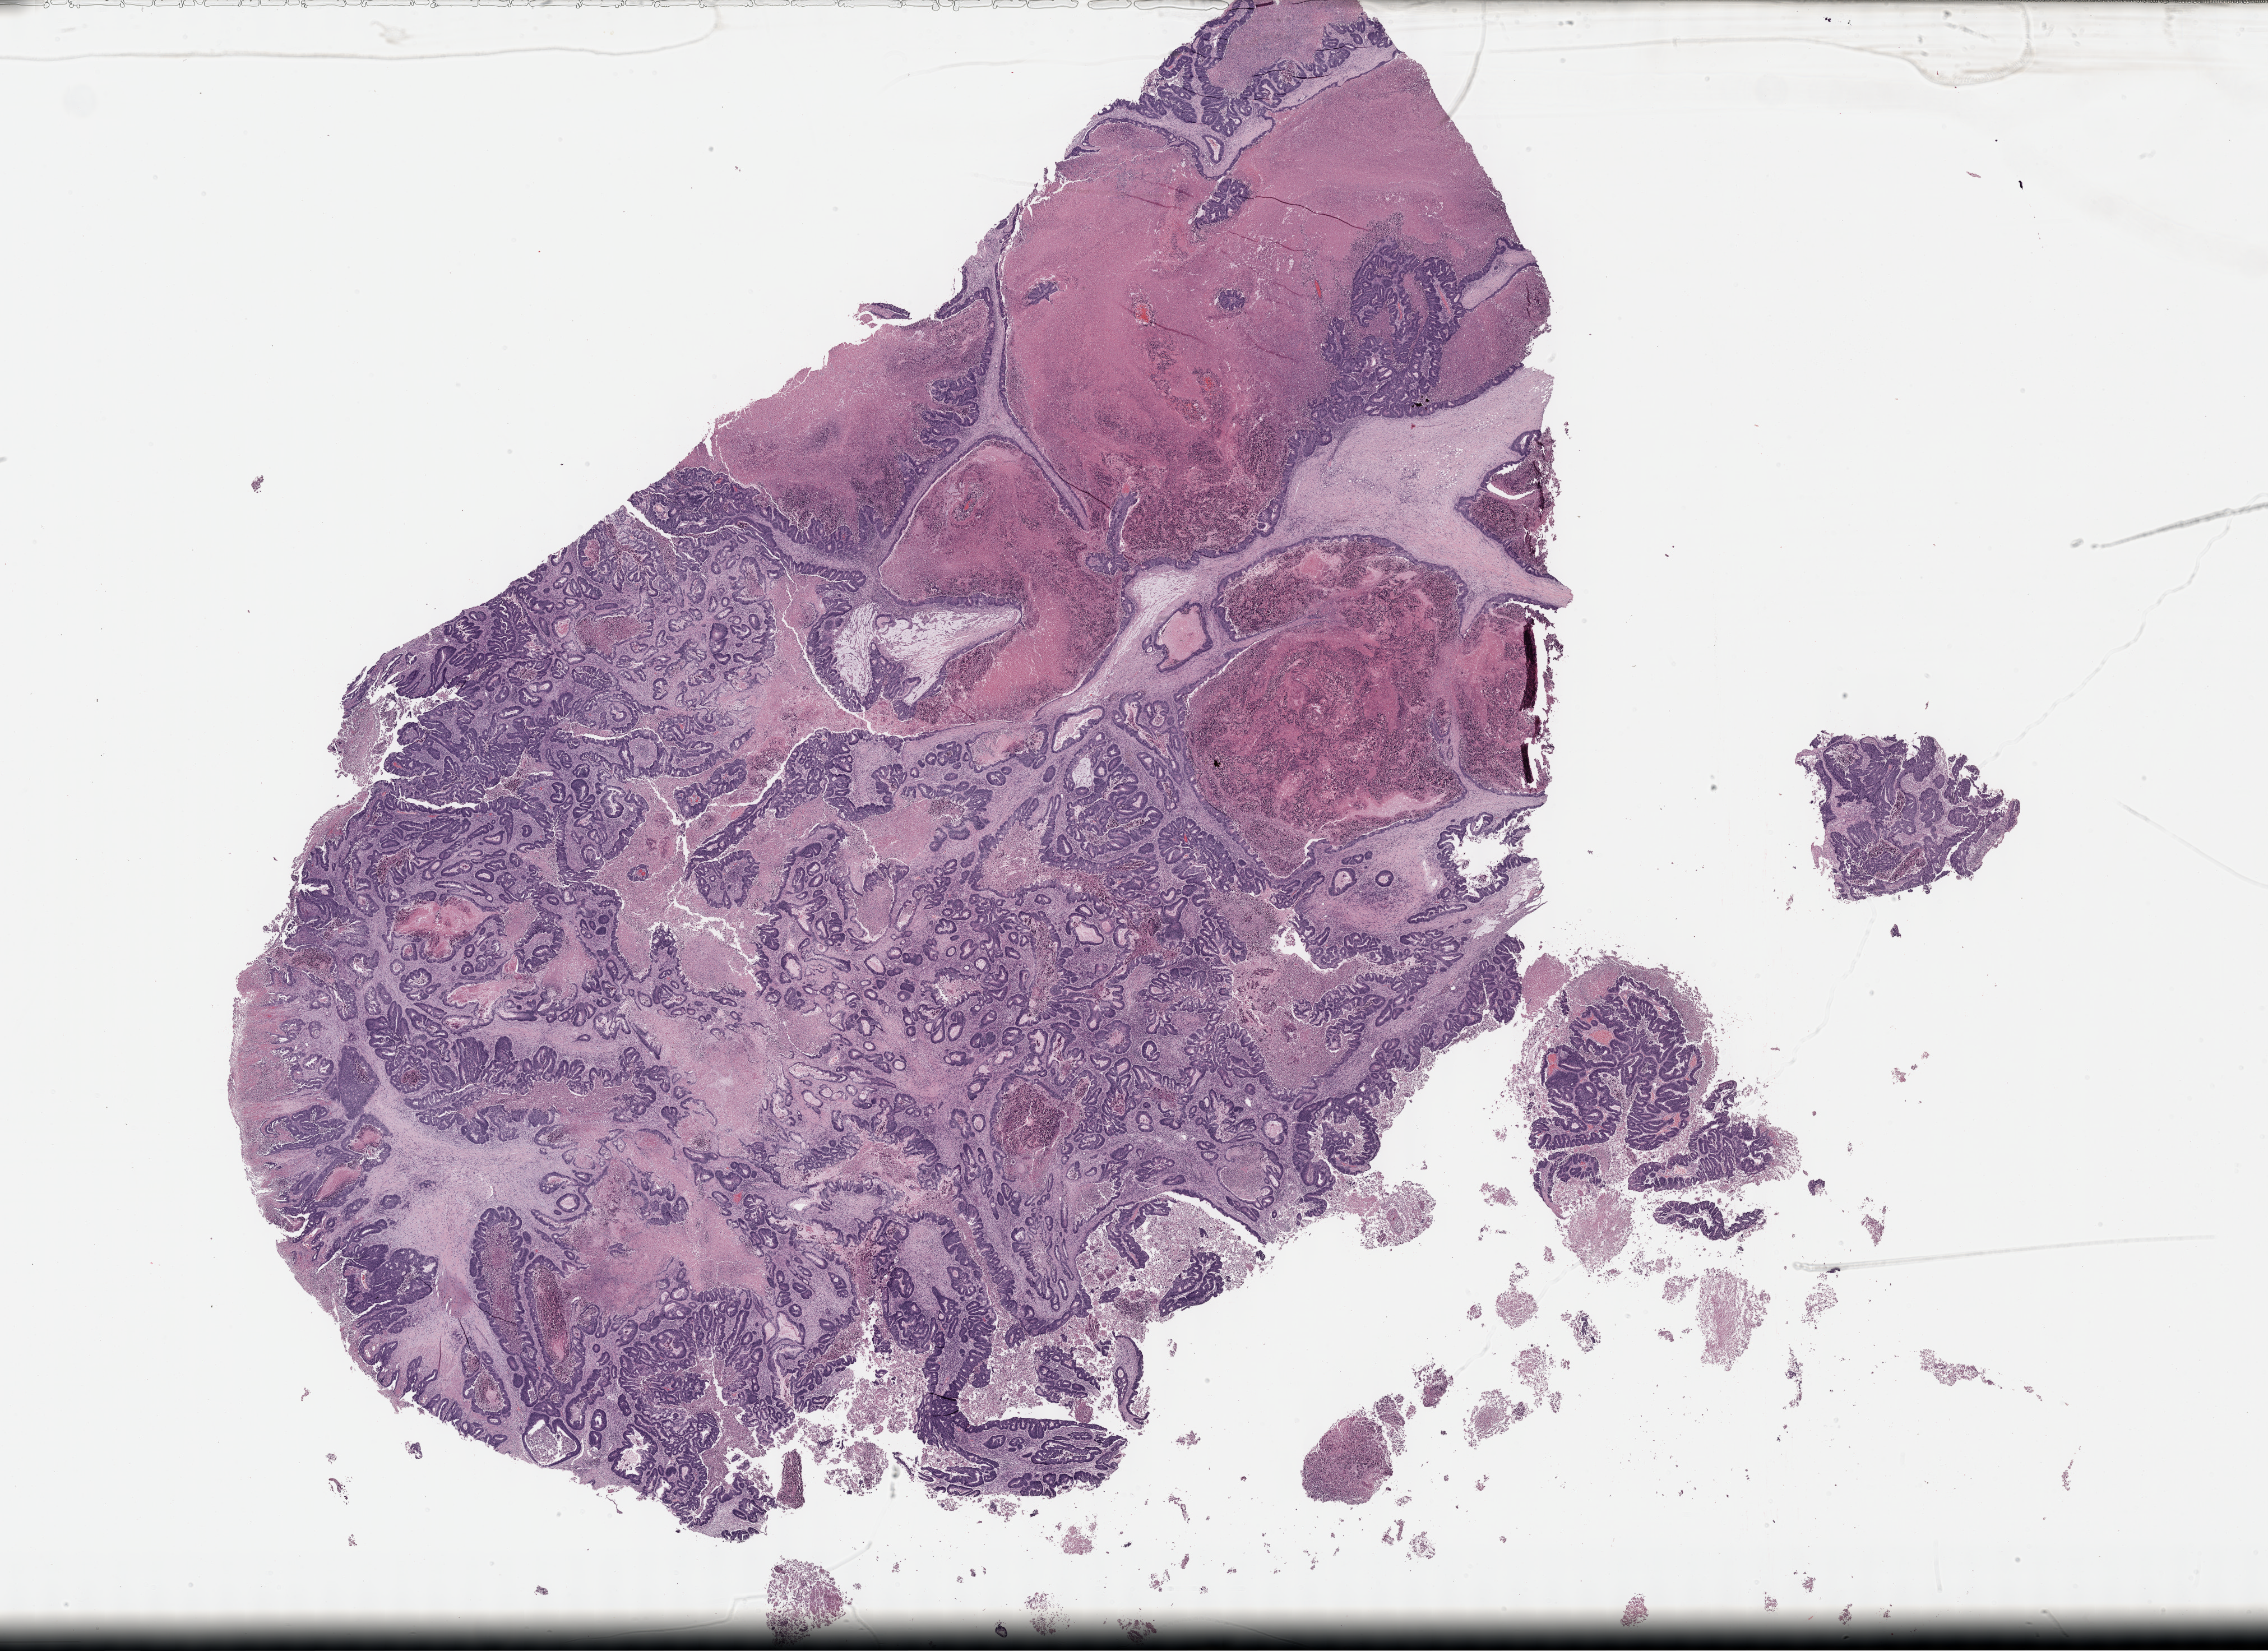
Digitized H&E-stained tissue section (whole slide) — low-resolution overview of the scanned area, about 32.7 x 23.8 mm (acquisition: 40x scan), formalin-fixed paraffin-embedded (FFPE) diagnostic section, primary tumour sample from the colon. Patient: female, age at initial diagnosis 64 years.
AJCC pathologic stage: IIIC (7th edition). Pathologic diagnosis: Adenocarcinoma, NOS (sigmoid colon). Lymph nodes positive (case pathology): 1 of 33 examined.